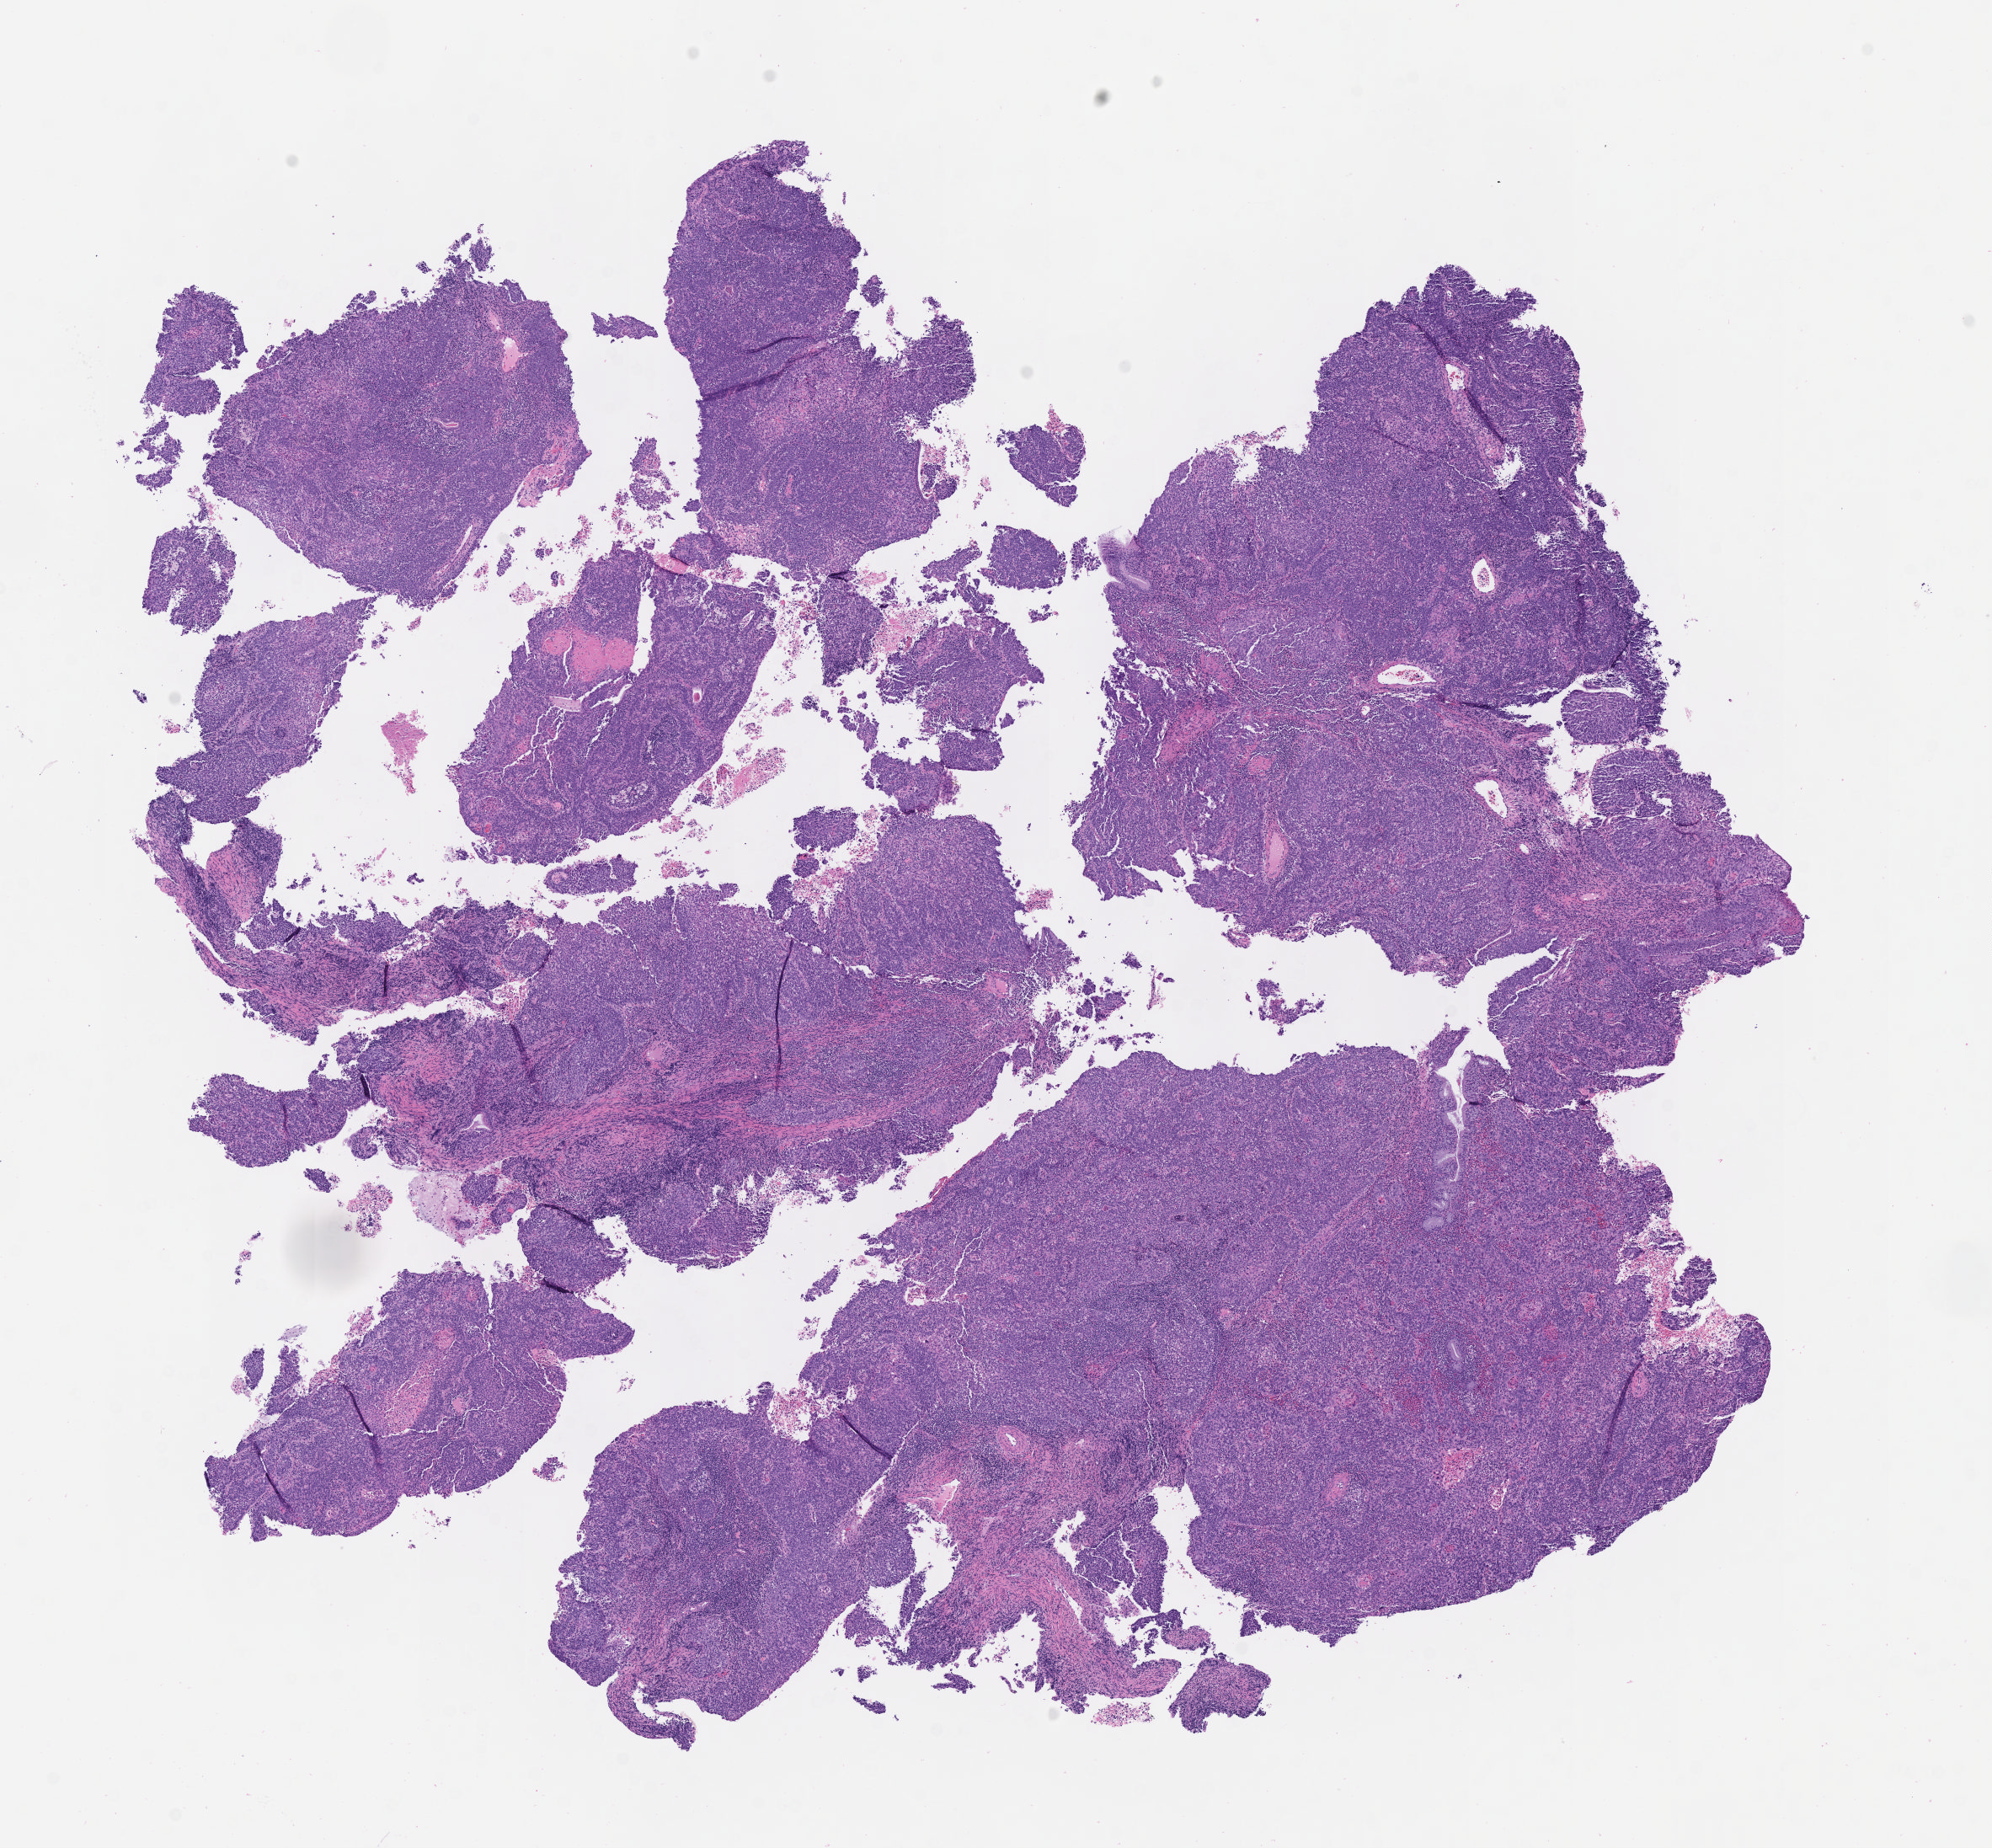
Whole-slide image, haematoxylin and eosin stain, shown as a low-resolution overview of the whole scanned area (about 9.6 x 8.9 mm), specimen: tumor tissue, anatomic site: cervix. Patient: female, 37 years old.
• histologic diagnosis: Lymphoepithelial carcinoma